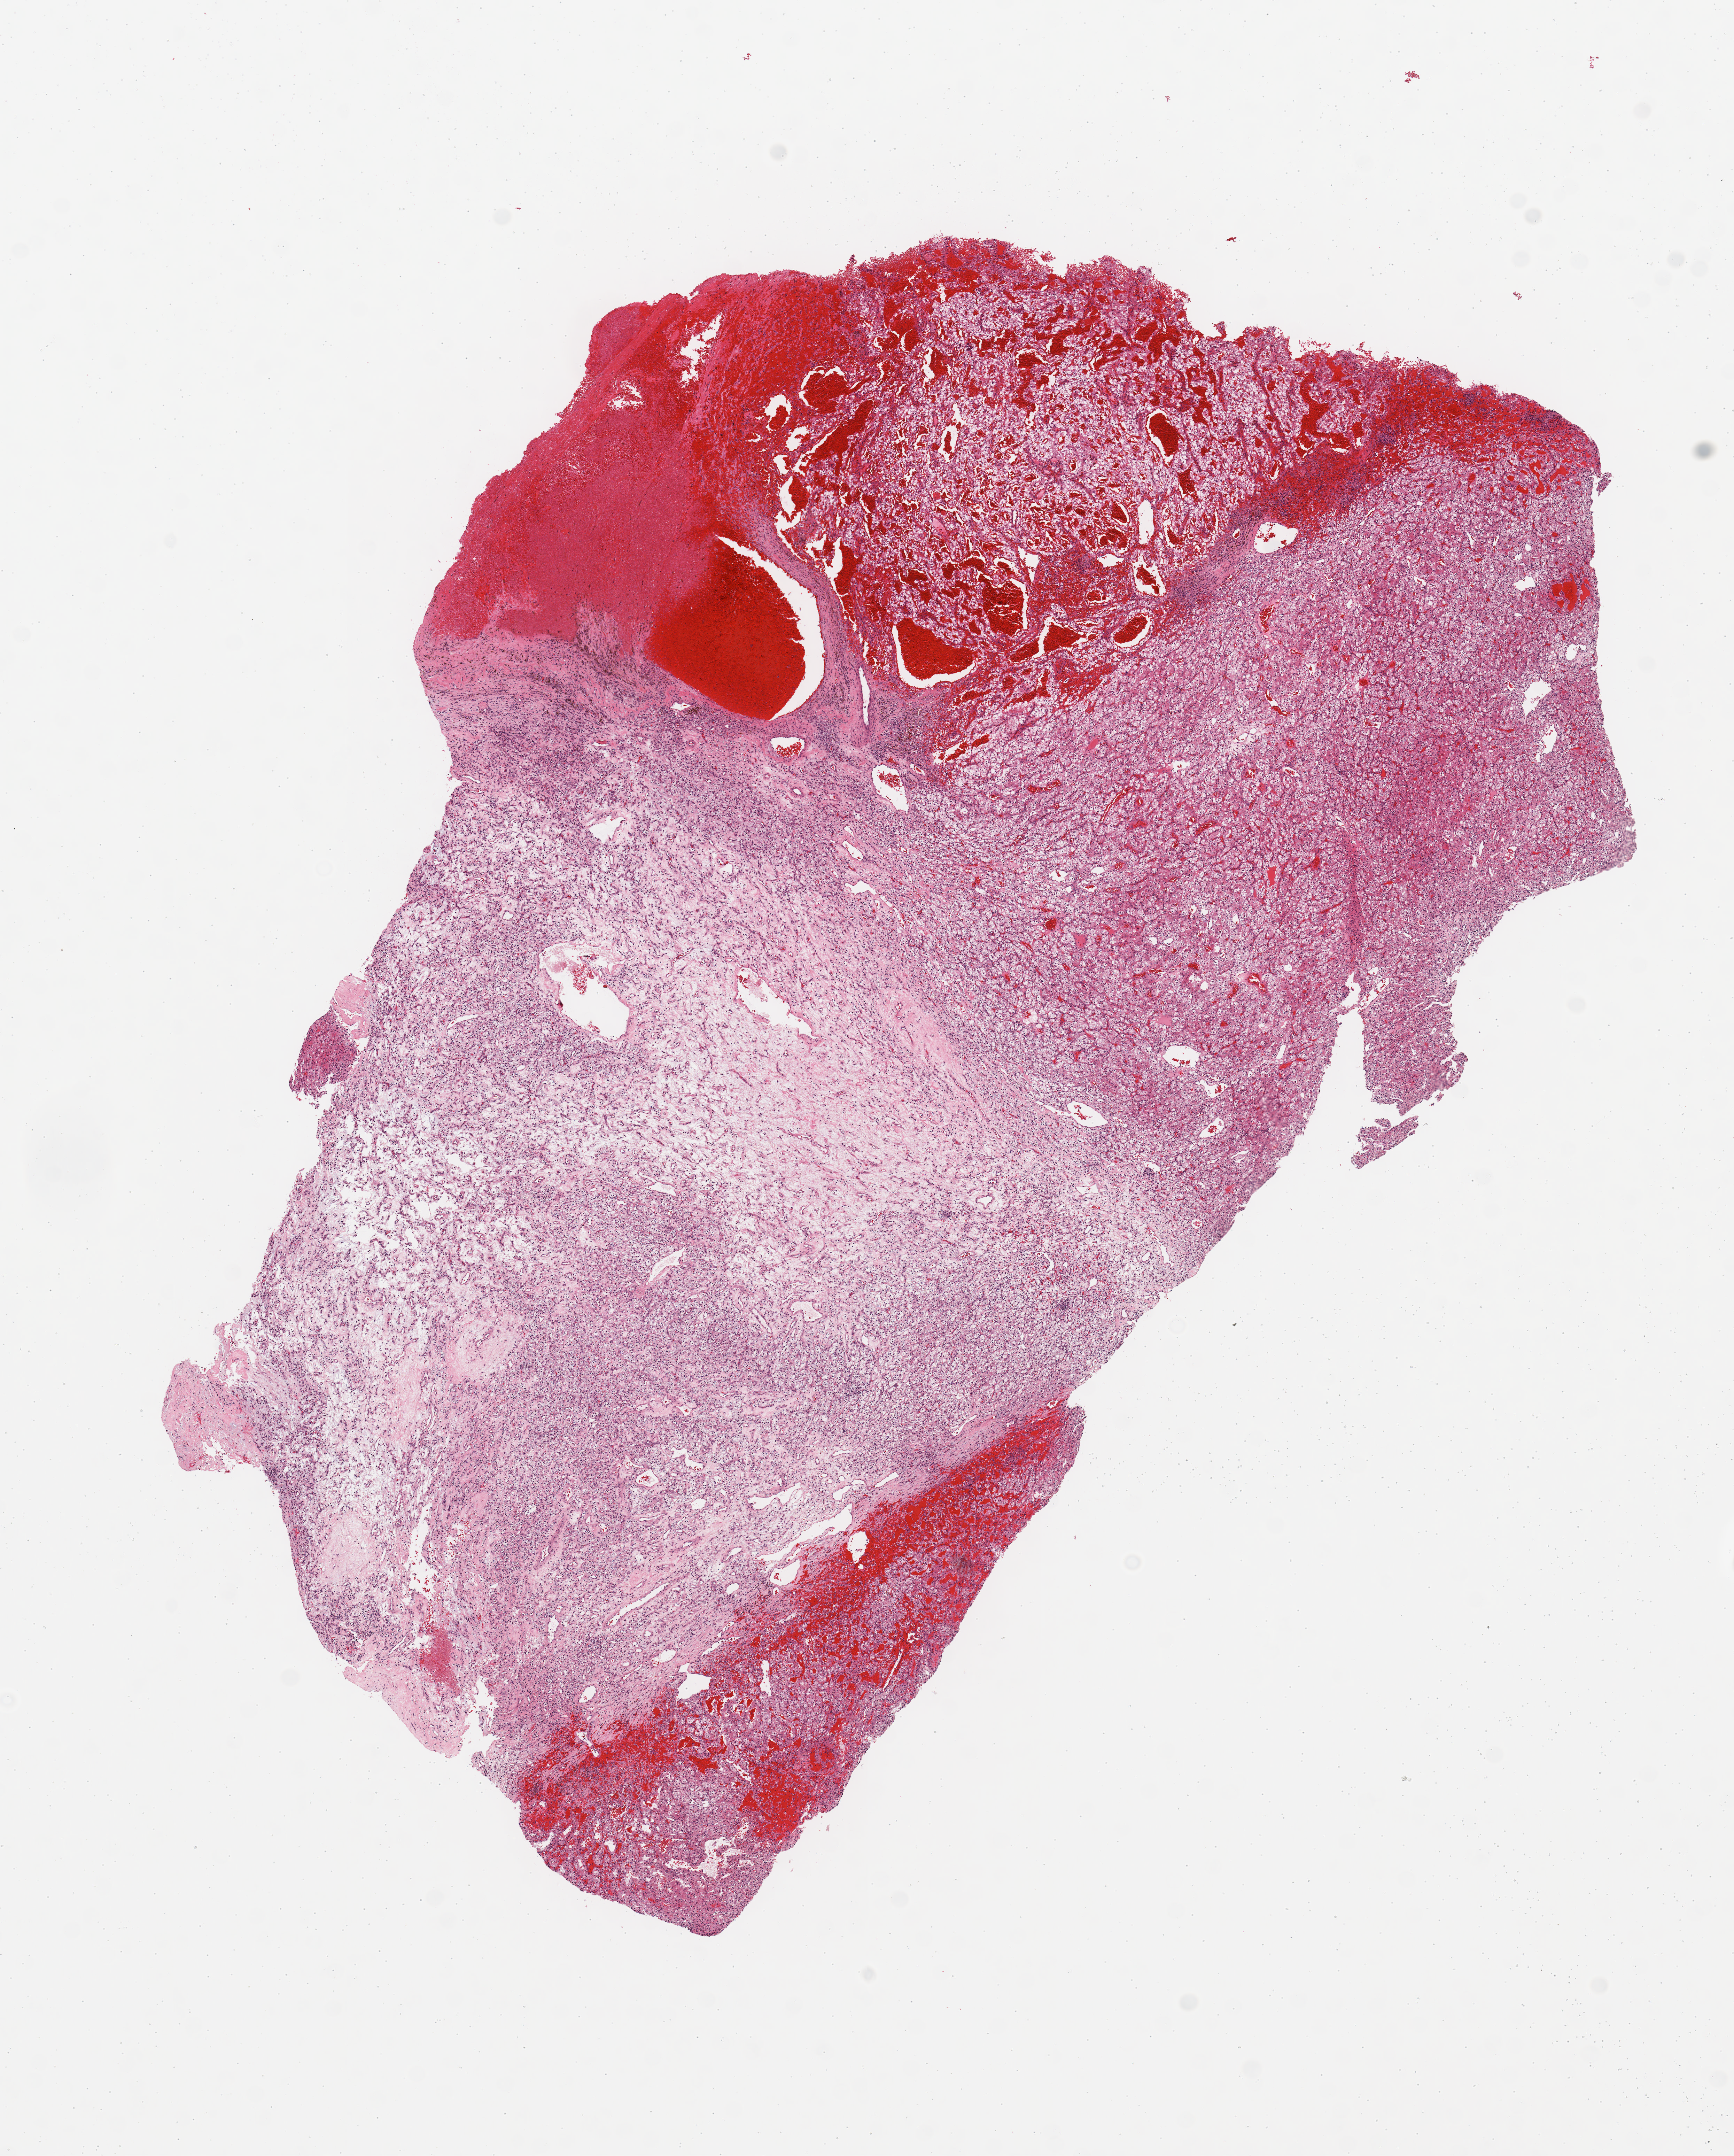
Hematoxylin and eosin (H&E) stained whole-slide image — whole scanned area (about 9.8 x 12.2 mm, slide scanned at 20x) shown as a low-resolution overview; tumour tissue sample, sampled site: kidney. Patient: female, age 75 years. Histologic grade: G3 (poorly differentiated). Composition of this section per pathologist review: tumour nuclei 85%, necrosis 5%.
AJCC pathologic stage: III. Histologic diagnosis: Renal cell carcinoma, NOS.